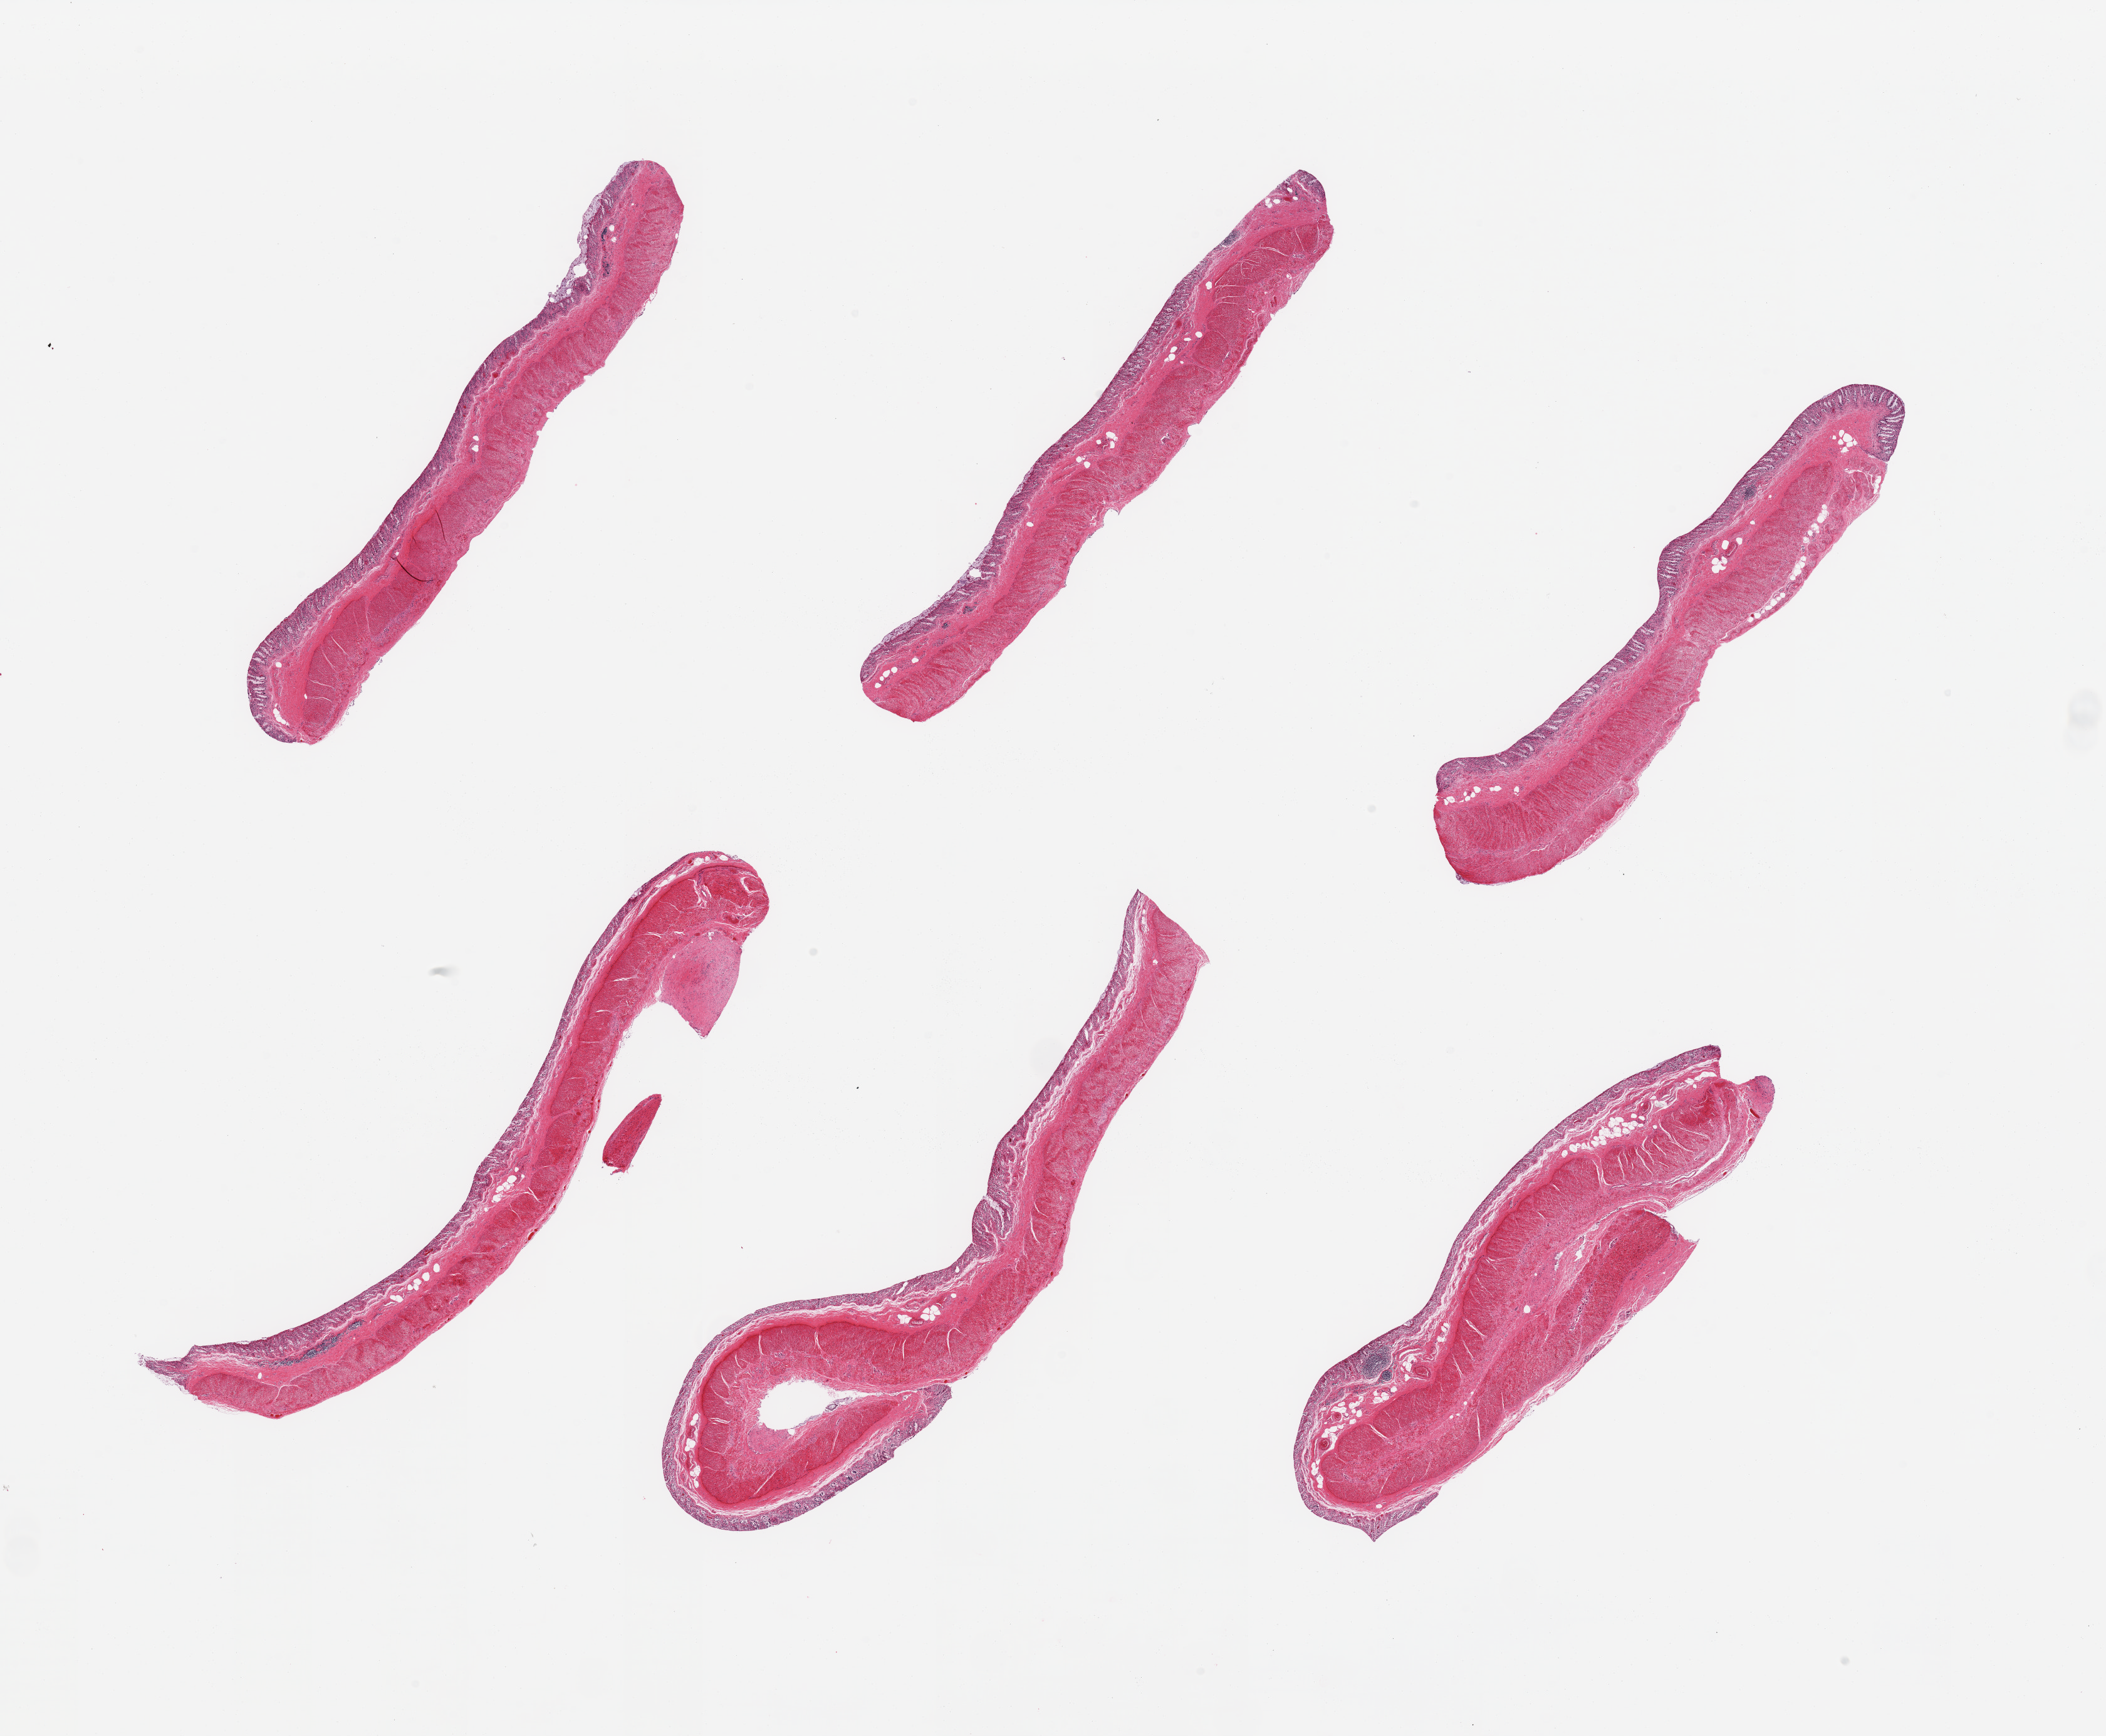
H&E whole-slide image — a low-resolution overview of the entire scanned area, about 26.6 x 21.9 mm. PAXgene-fixed, paraffin-embedded tissue. Section of transverse colon (target tissue). Donor tissue sample.
Pathologist's review note for this sample: 6 pieces; moderate to severe mucosal autolysis; preserved muscularis; congested serosa.